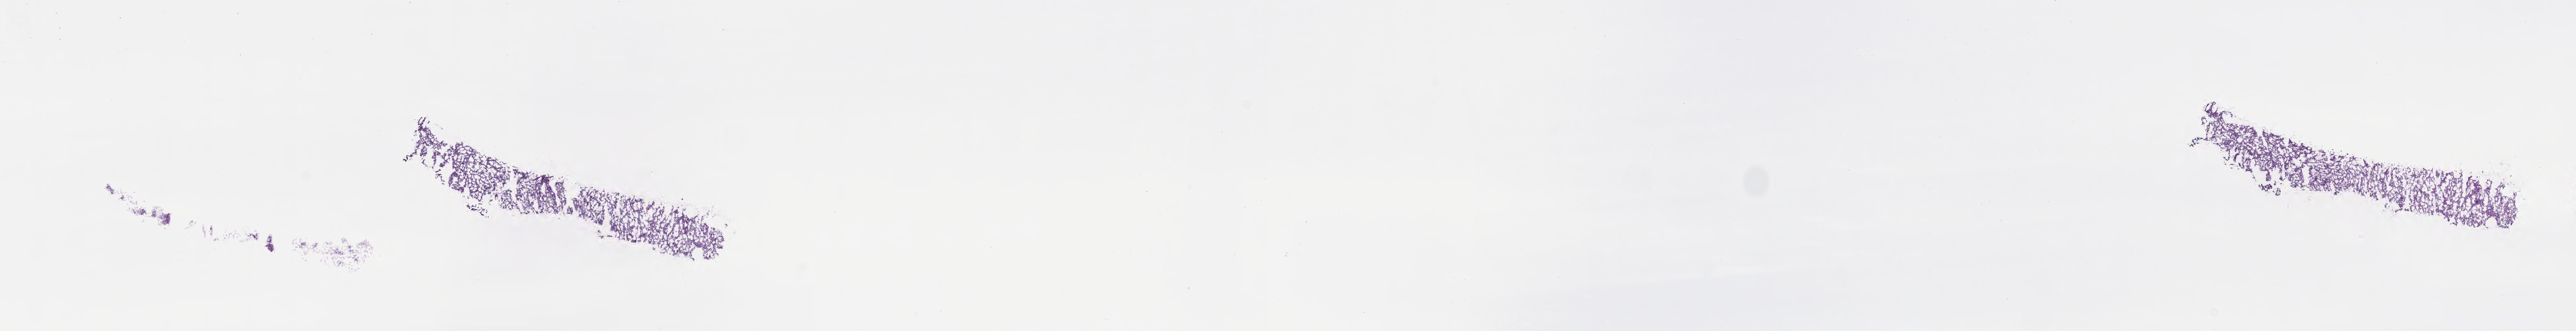
H&E whole-slide image of tumor tissue from the orbit, whole scanned area (about 30.7 x 3.9 mm) shown as a low-resolution overview. Frozen section. Patient male; age 68 months (5 years 8 months).
- recorded diagnosis: Embryonal rhabdomyosarcoma, NOS